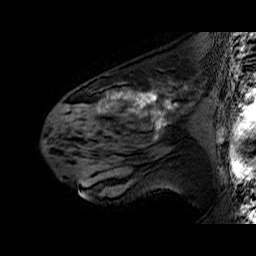
Breast MRI (dynamic contrast-enhanced), one sagittal slice. Slice 37 of 60 in the series (ordered by position). Dynamic contrast-enhanced series, time point 2 of 6 at this slice position (early post-contrast). 1.5 T. TE 6.4 ms, TR 32.9 ms. 256 × 256 image matrix. Female patient. From the clinical record (not read from this slice): setting: breast cancer imaged before/during neoadjuvant chemotherapy; receptor status: HER2-positive.
Annotated regions visible in this slice (semi-automatic segmentation, software-assisted and operator-edited):
- analysis volume of interest (the breast-tissue region the enhancement analysis was run in; not a lesion): bounding box [x1, y1, x2, y2] px = [51, 78, 196, 160]
- tumour enhancement mask (voxels above the 100 % enhancement threshold inside the analysis volume of interest): [79, 91, 172, 137]